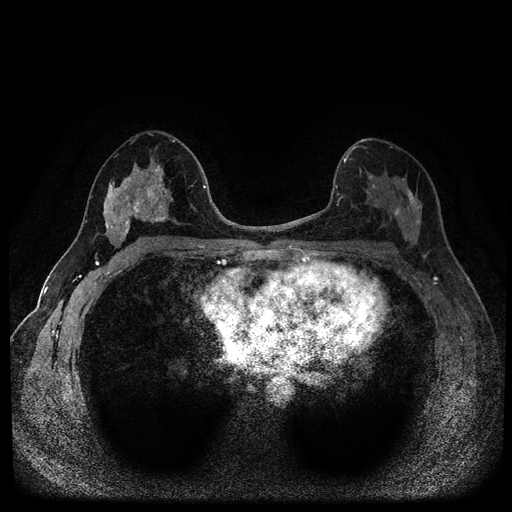
Breast MRI (dynamic contrast-enhanced, multi-phase), one axial slice. Slice 55 of 116 in the series (ordered by position). Dynamic contrast-enhanced series, time point 2 of 5 at this slice position (early post-contrast). 1.5 T. TE 2.7 ms, TR 5.4 ms. 2 mm slice thickness. 512 × 512 image matrix. Female patient, age 49 years.
Outlined on this slice (semi-automatic segmentation, software-assisted and operator-edited):
- breast lesion (labelled benign in the annotation): bounding box <103,161,171,248> (left, top, right, bottom; pixels)